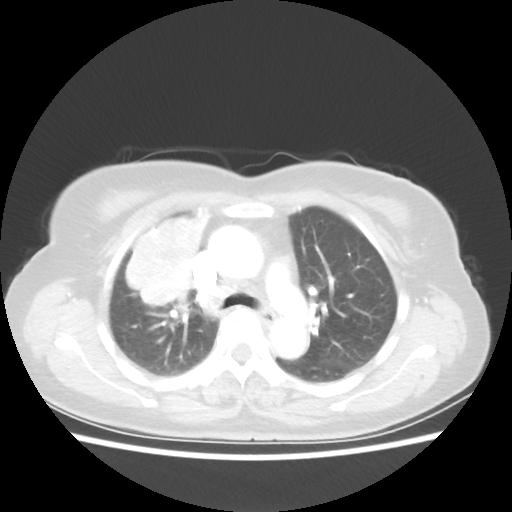
Chest CT, one axial slice; position 36 of 55 along the scan axis; lung window (W 1500 / L -600 HU); 5 mm slice thickness; 512 × 512 image matrix. Female patient, age 62 years. From the clinical record (not read from this slice): clinical TNM (as recorded): T4 N3 M0.
Annotated regions visible in this slice (bounding box drawn by a radiologist):
- lung tumour (recorded histology: squamous cell carcinoma): bounding box [x1, y1, x2, y2] px = [118, 205, 214, 314]